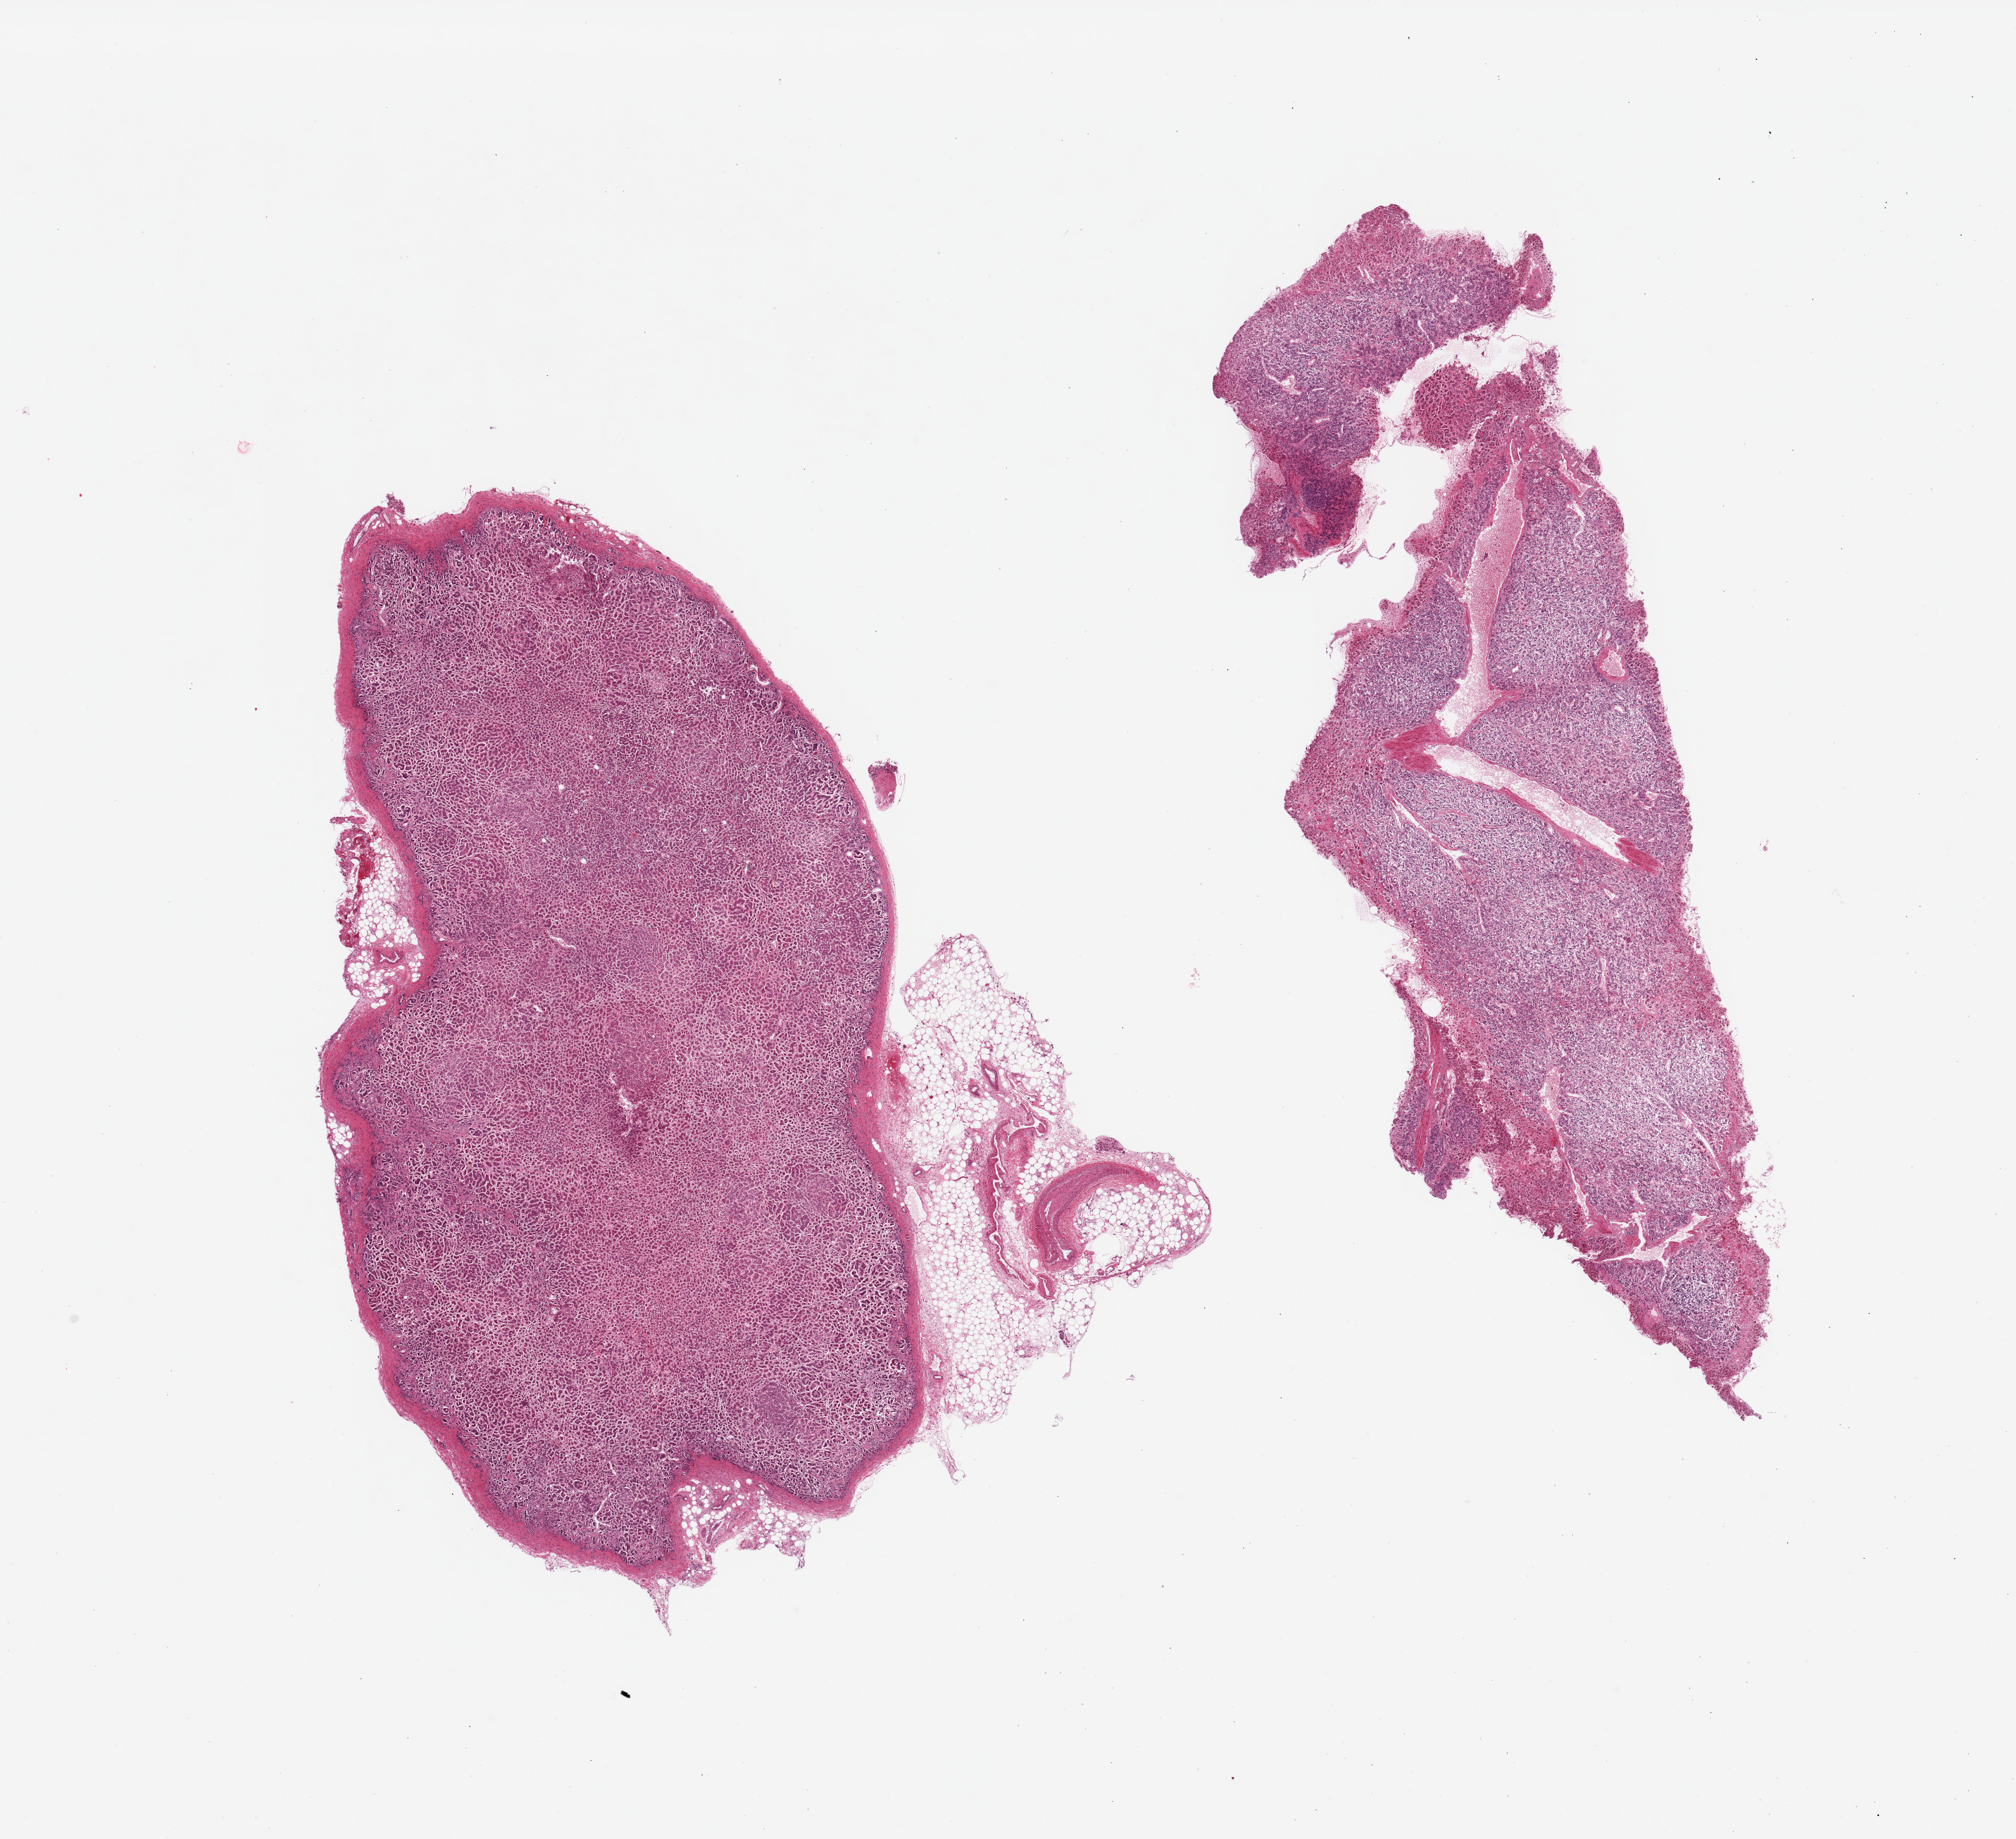
H&E whole-slide image — low-resolution overview of the scanned area, about 22.6 x 20.7 mm, PAXgene-fixed paraffin-embedded (PFPE) section, target tissue: adrenal gland, tissue donor sample.
Reviewer comment on this tissue sample: 2 pieces; cortex; no internal fat; small amount of adherent externa; fat.